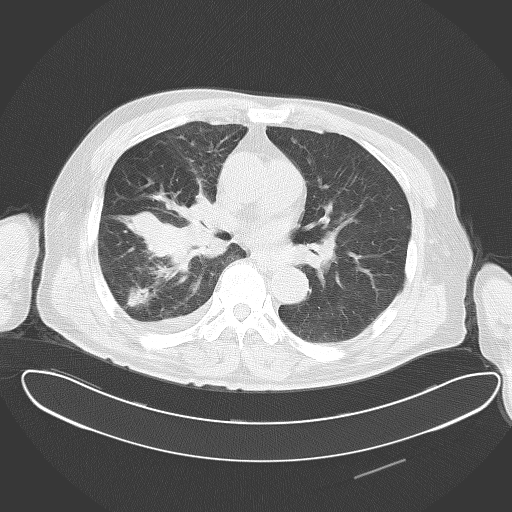
Chest CT, one axial slice. Position 30 of 62 along the scan axis. Reconstruction kernel B70f. 120 kVp. Lung window (W 1500 / L -600 HU). 5 mm slice thickness. 512 × 512 image matrix, field of view 427 × 427 mm. Male patient, age 78 years. From the clinical record (not read from this slice): clinical TNM (as recorded): T2 N1 M1.
Annotated regions visible in this slice (bounding box drawn by a radiologist):
- lung tumour (recorded histology: adenocarcinoma): bounding box <121,183,225,273> (left, top, right, bottom; pixels)